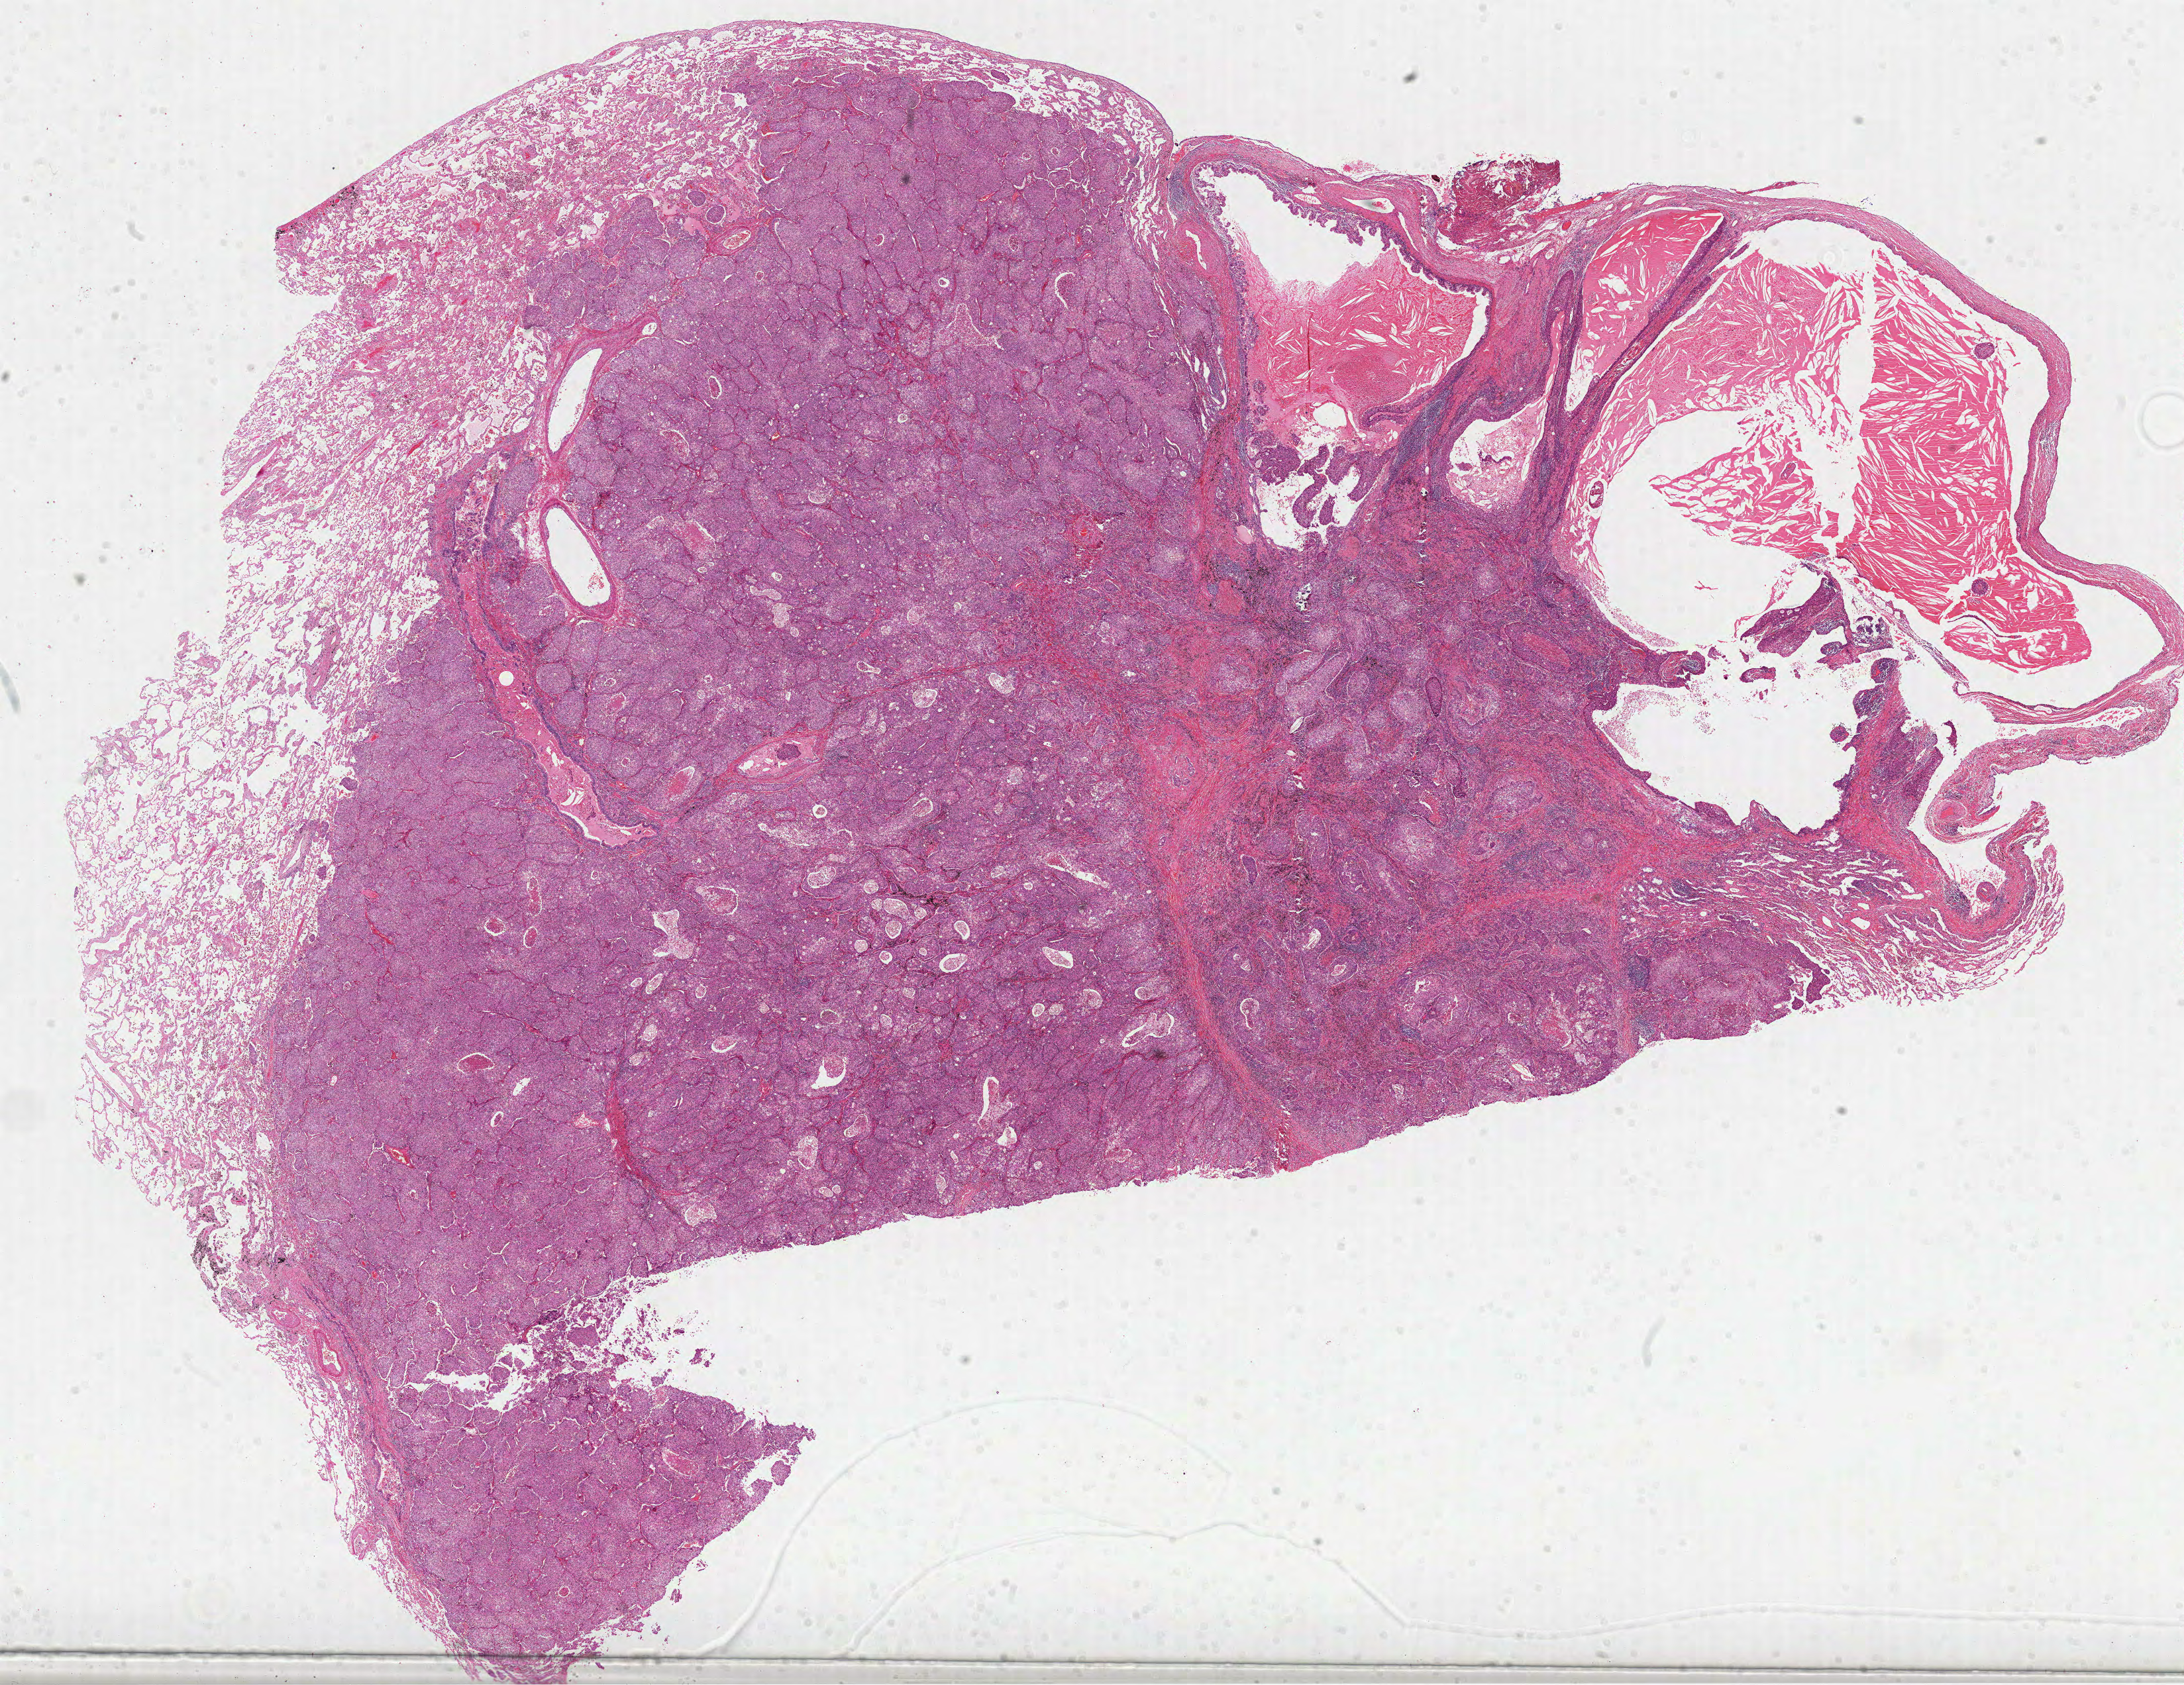
H&E whole-slide image, whole scanned area (about 26.6 x 20.5 mm, from a 40x scan) shown as a low-resolution overview, formalin-fixed paraffin-embedded (FFPE) diagnostic section, lung, primary tumour sample. Patient: female, age at initial diagnosis 53 years.
- histologic diagnosis: Adenocarcinoma with mixed subtypes (upper lobe, lung)
- TNM: T2 N2 M0
- laterality: left
- AJCC pathologic stage: IIIA